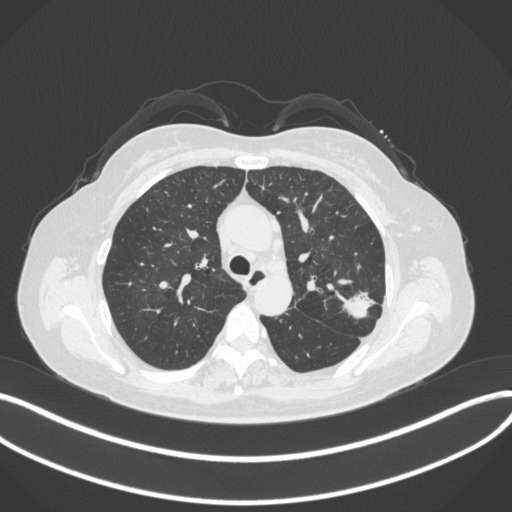
Chest CT, one axial slice. Position 237 of 330 along the scan axis. Reconstruction kernel B31f. 120 kVp. Lung window (W 1500 / L -600 HU). 1 mm slice thickness. 512 × 512 image matrix. Patient: female, 60 years. From the clinical record (not read from this slice): clinical TNM (as recorded): T1c N0 M0.
Annotated regions visible in this slice (rectangle marked by the reading radiologist):
- lung tumour (recorded histology: adenocarcinoma): bounding box [x1, y1, x2, y2] px = [336, 284, 374, 324]